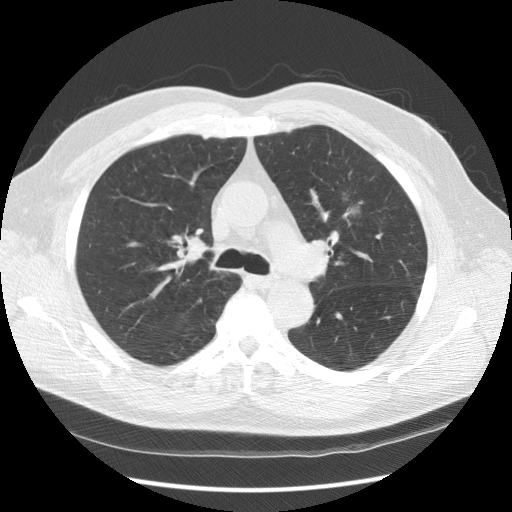
Low-dose screening chest CT, one axial slice. Slice 102 of 157 in the series (ordered by position). Reconstruction kernel STANDARD. Lung window (W 1500 / L -600 HU). 2.5 mm slice thickness. 512 × 512 image matrix, field of view 370 × 370 mm.
Outlined on this slice (expert manual segmentation):
- lesion 1 (tumor, upper lobe of left lung): bounding box <344,209,355,218> (left, top, right, bottom; pixels)